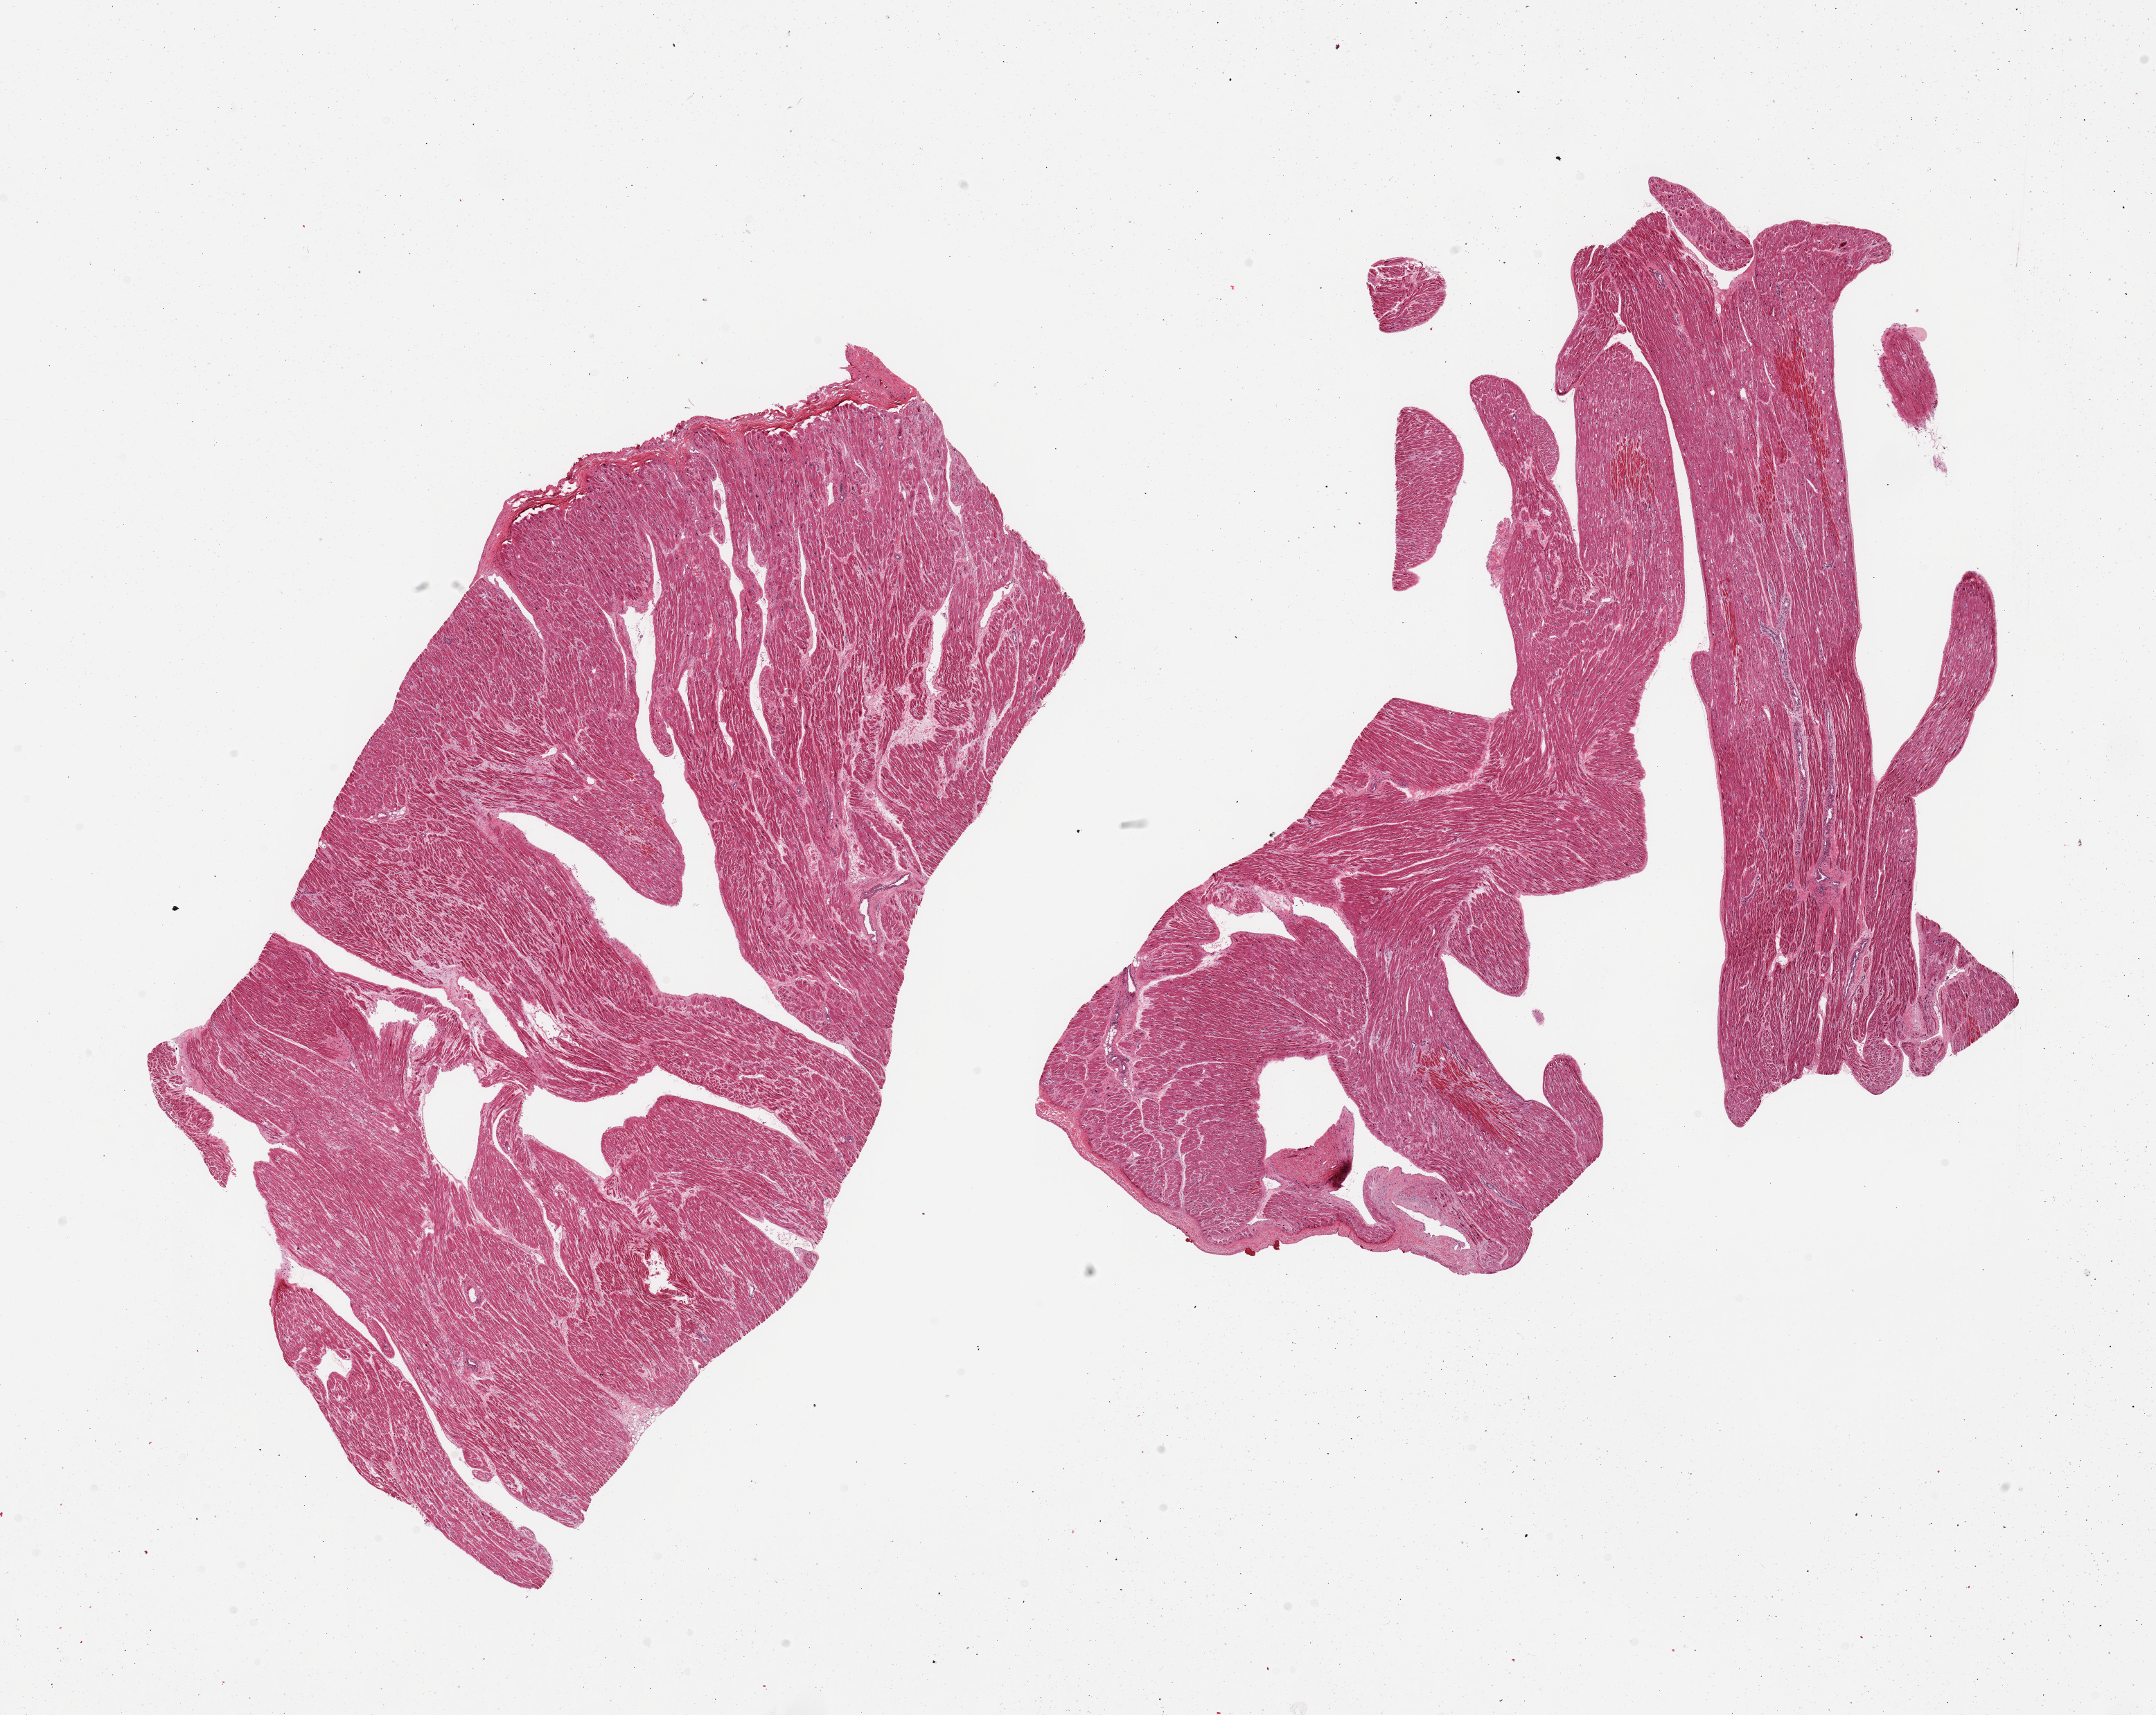
Digitized hematoxylin and eosin (H&E)-stained section, a low-resolution overview of the entire scanned area, about 24.6 x 19.6 mm (slide scanned at 20x), PAXgene-fixed paraffin-embedded (PFPE) section, sampled site (target tissue): auricular appendage, donor tissue sample. Male donor.
Review note (as recorded): 2 pieces; foci of hypereosinophilia (ischemic).